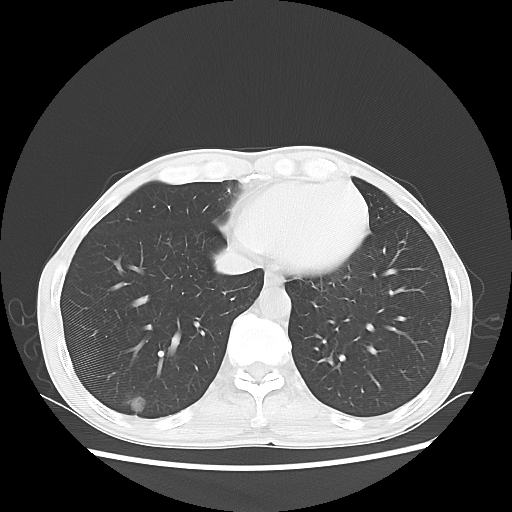
Chest CT, one axial slice; position 20 of 68 along the scan axis; reconstruction kernel LUNG; 100 kVp; lung window (W 1500 / L -600 HU); 5 mm slice thickness; 512 × 512 image matrix, field of view 360 × 360 mm. Male patient, age 60 years. From the clinical record (not read from this slice): clinical TNM (as recorded): T1c N0 M0.
Structures marked on this image (rectangle marked by the reading radiologist):
- lung tumour (recorded histology: adenocarcinoma): box from (x=121, y=395) to (x=151, y=418) px